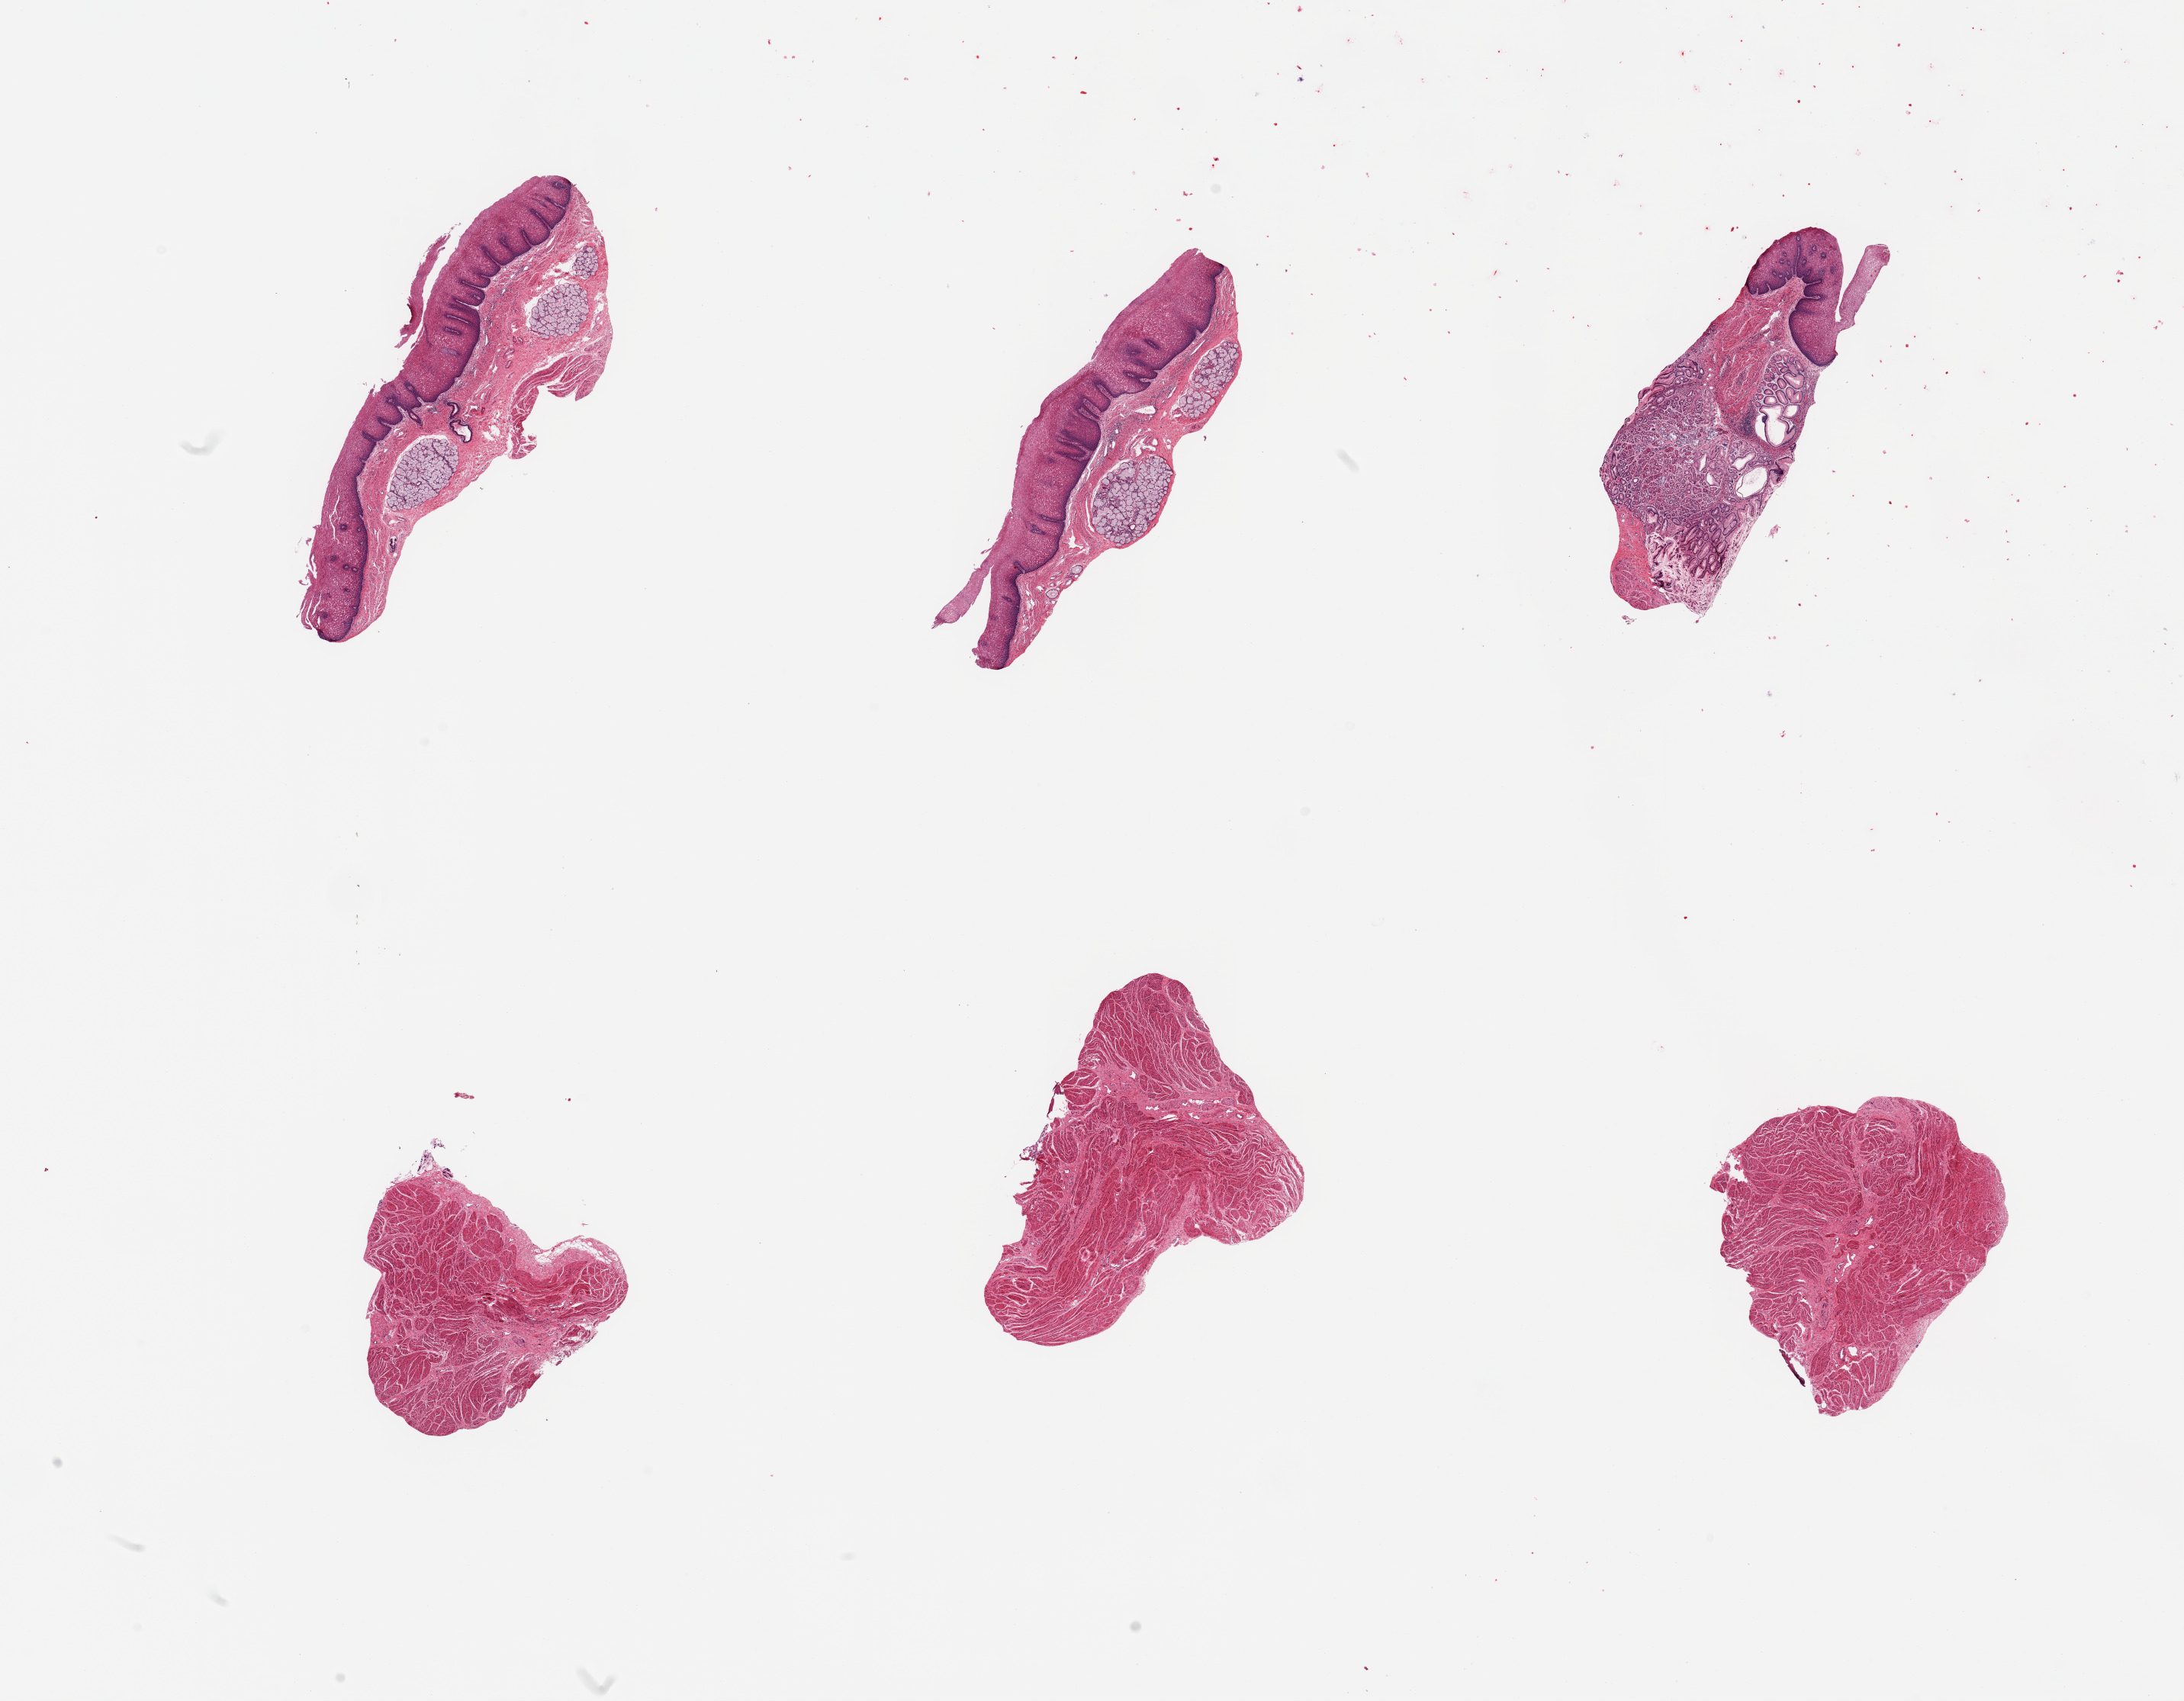
Digitized hematoxylin and eosin (H&E)-stained section — low-resolution overview of the scanned area, about 22.6 x 17.6 mm. PAXgene-fixed, paraffin-embedded tissue. Sampled site (target tissue): gastroesophageal junction. Donor tissue sample.
- reviewer comment on this tissue sample: 6 pieces; 3 are mucosa, 3 are muscularis